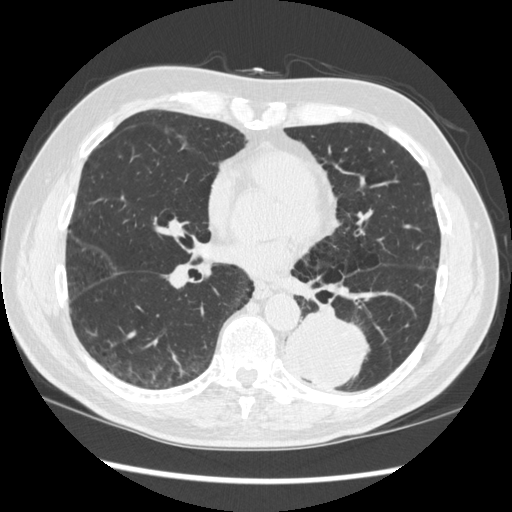
Low-dose screening chest CT, one axial slice; position 150 of 348 along the scan axis; reconstruction kernel STANDARD; 120 kVp; lung window (W 1500 / L -600 HU); 1.25 mm slice thickness; 512 × 512 image matrix.
Annotated regions visible in this slice (manually delineated by an expert):
- lesion 1 (tumor, lower lobe of left lung): bounding box <285,313,368,390> (left, top, right, bottom; pixels)